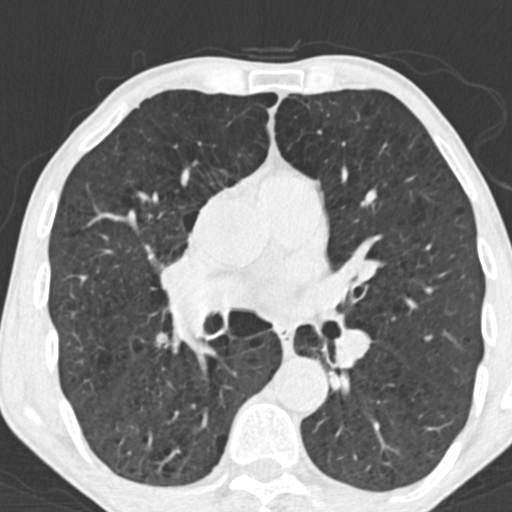
Chest CT (low-dose screening protocol), one axial image; baseline screening round; lung window (W 1500 / L -600 HU); slice 91 of 180 in the series; 512 × 512 image matrix, field of view 286 × 286 mm. Male participant, aged 64 years at enrolment. Current smoker at enrolment.
• Expert reader's lesion annotation, bounding box <139,320,190,365> (left, top, right, bottom; pixels).
• Screening reader's record for this exam: no non-calcified nodule ≥4 mm recorded.